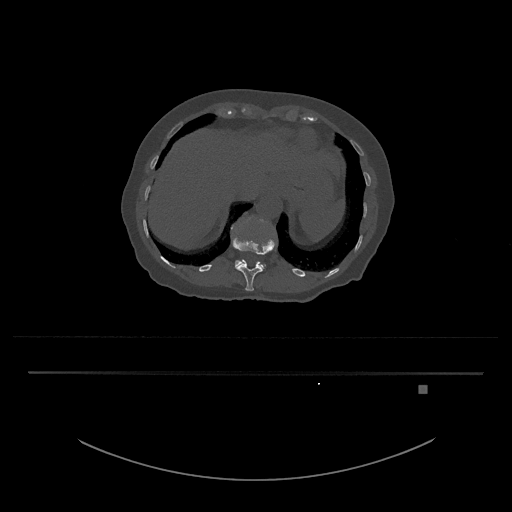
CT including the spine, one axial slice. Position 595 of 797 along the scan axis. Reconstruction kernel Br40s/3. 120 kVp. Bone window (W 1800 / L 400 HU). 0.5 mm slice thickness. 512 × 512 image matrix, field of view 500 × 500 mm. Female patient, age 57 years. From the clinical record (not read from this slice): primary cancer: cervical.
Structures marked on this image (semi-automatically segmented with operator editing):
- L1 vertebra: box from (x=235, y=260) to (x=266, y=270) px
- T12 vertebra: (x=231, y=234)–(x=275, y=291)